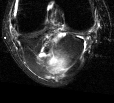
MRI of an extremity soft-tissue mass, one axial slice. Slice 11 of 44 in the series (ordered by position). T2-weighted fat-saturated. MR volume resampled by the dataset authors to the PET/CT grid (not the native acquisition matrix). 3.27 mm slice thickness. 114 × 103 image matrix, field of view 111 × 101 mm. Female patient. Case-level facts recorded for this patient, not image findings: histological type: liposarcoma; site of the primary tumour: right thigh.
Outlined on this slice (expert contour drawn on MRI and transferred to this co-registered scan by the dataset authors):
- gross tumour volume (mass): bounding box (x1, y1, x2, y2) in pixels: (45, 55, 66, 74)